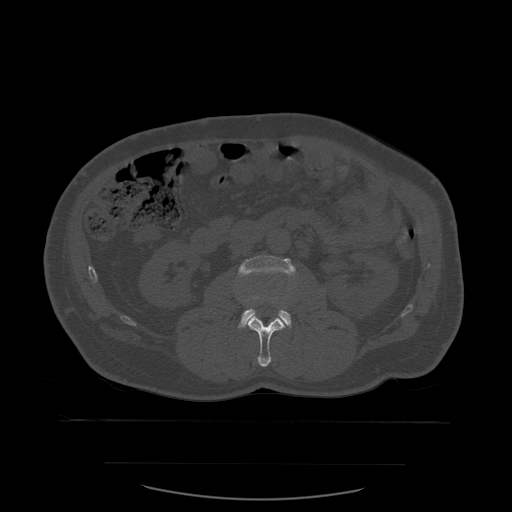
CT including the spine, one axial slice; slice 207 of 590 in the series (ordered by position); bone window (W 1800 / L 400 HU); 1.25 mm slice thickness; 512 × 512 image matrix, field of view 479 × 479 mm. Patient age 71 years. From the clinical record (not read from this slice): primary cancer: lung; vertebrae with lytic lesions (as recorded): T1, T2, L5, S1.
Annotated regions visible in this slice (semi-automatically segmented with operator editing):
- L2 vertebra: bounding box <244,297,290,367> (left, top, right, bottom; pixels)
- L3 vertebra: <238,255,296,329>